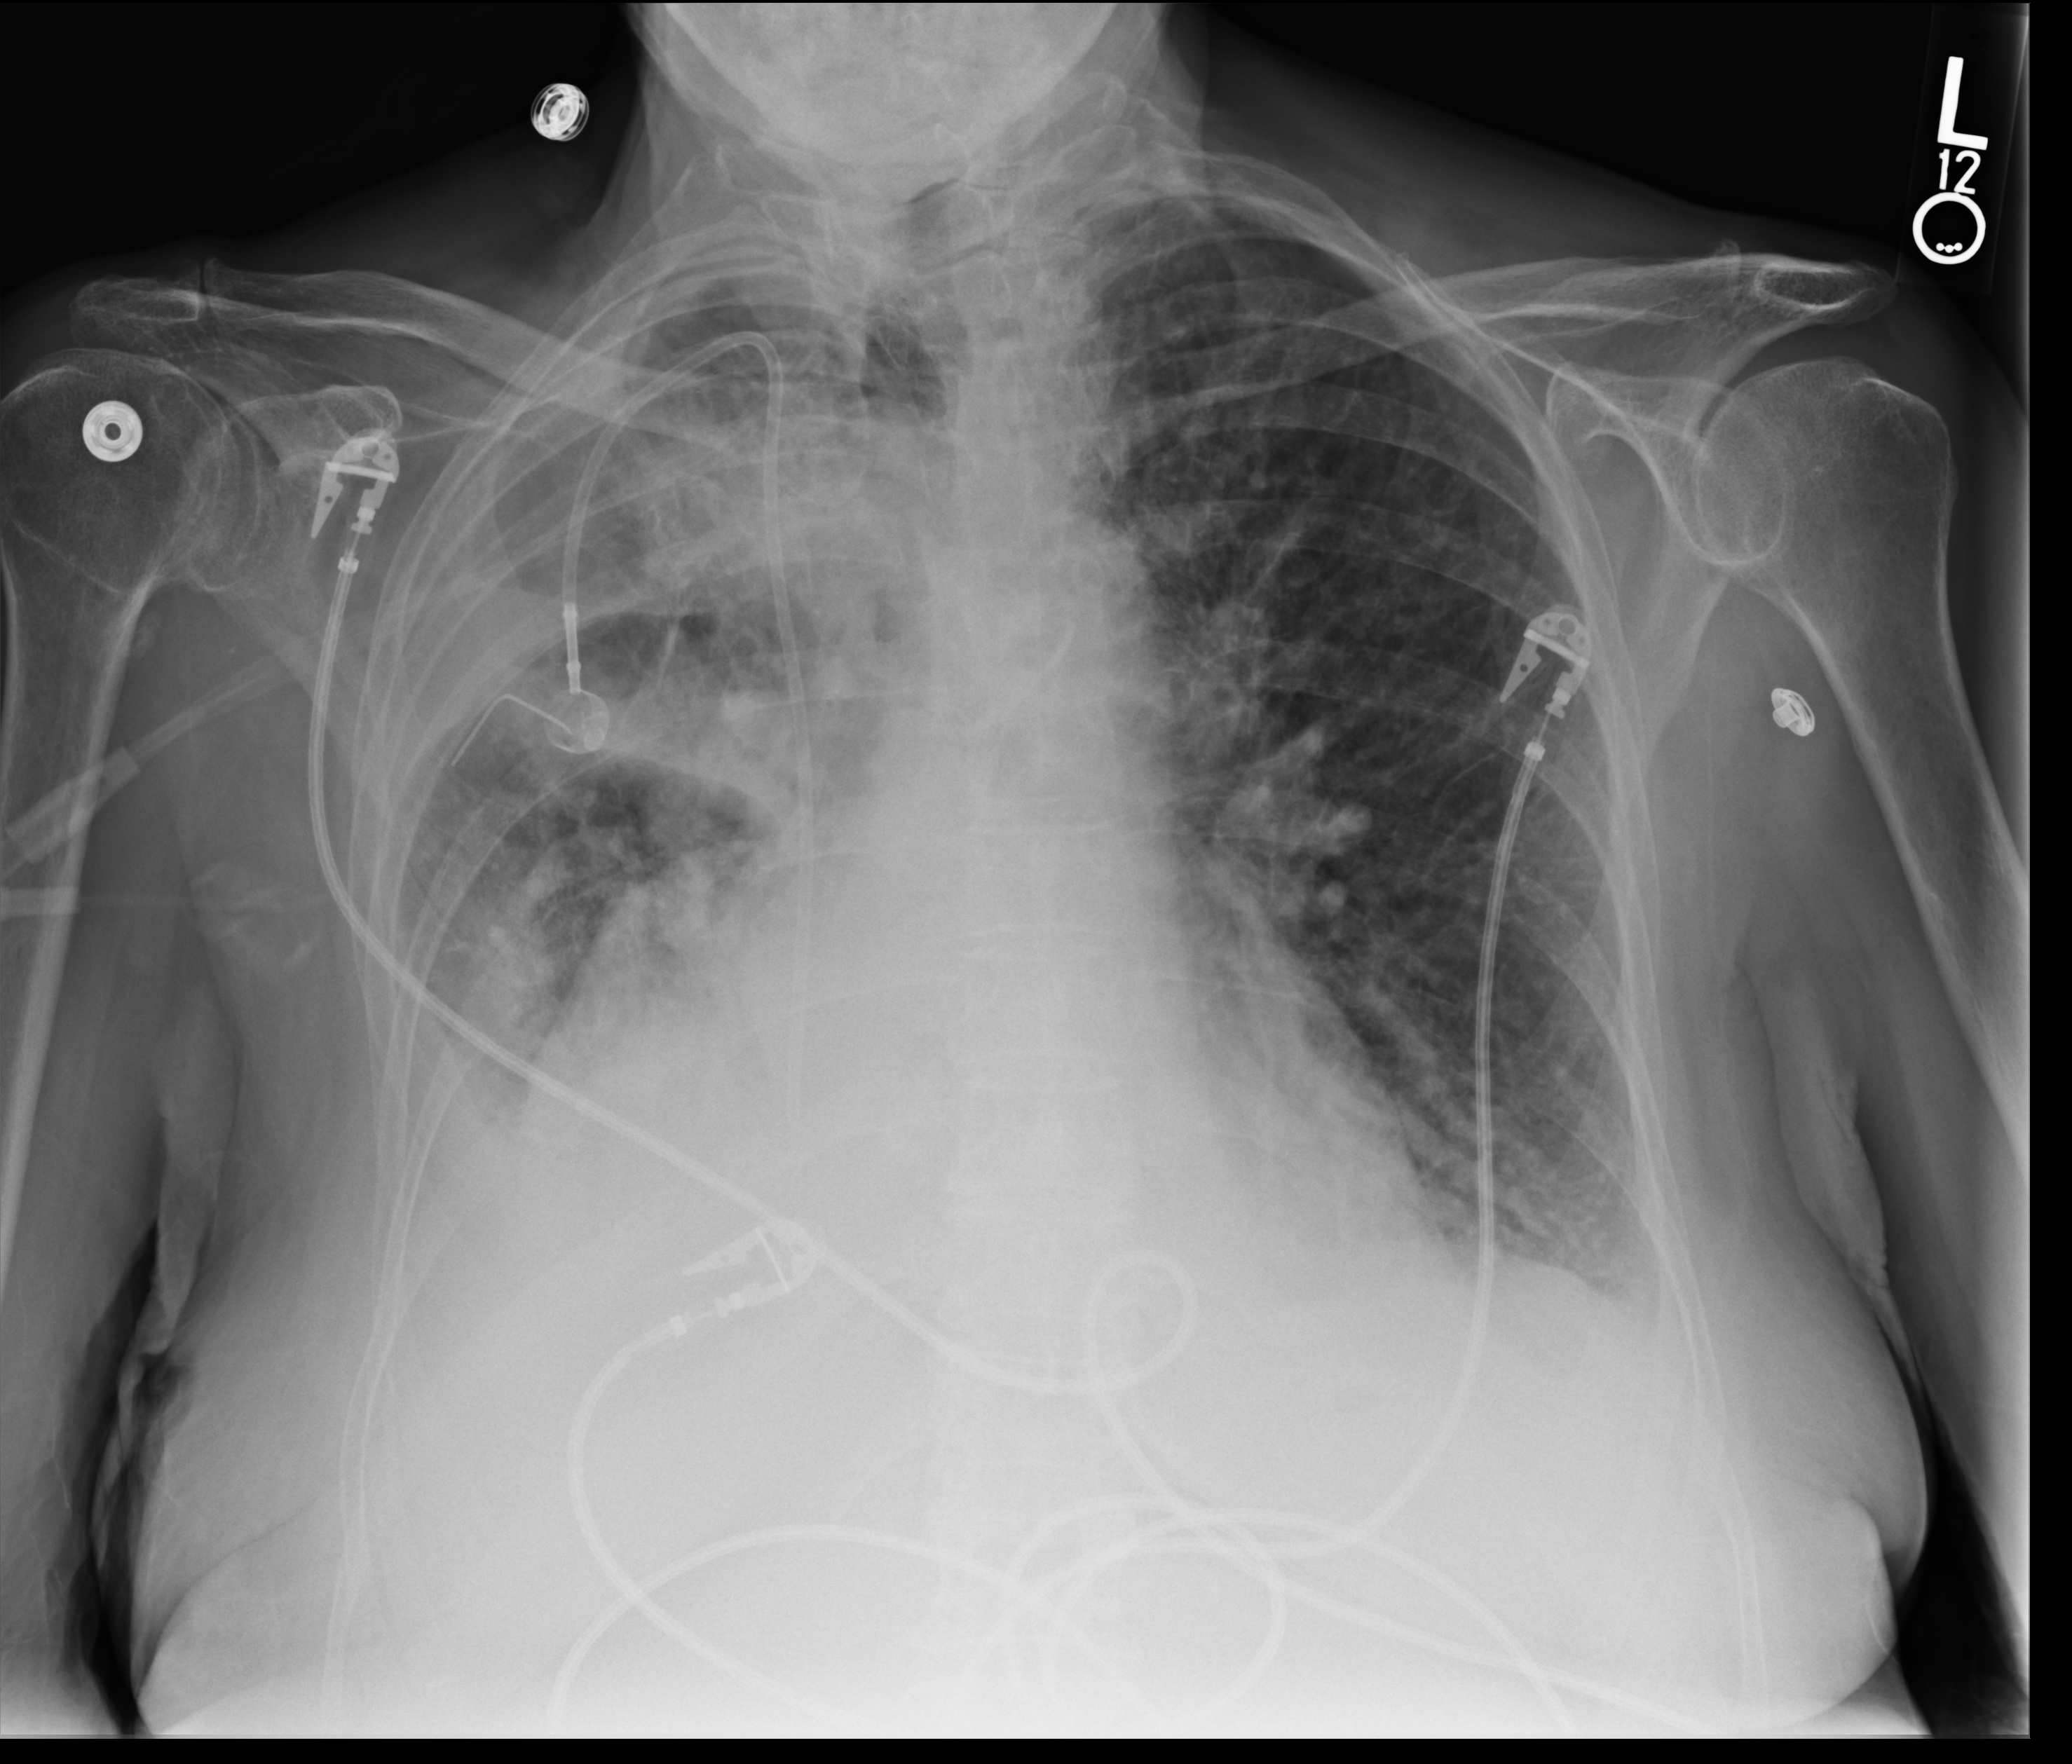
Portable chest radiograph, anteroposterior (AP) projection. Female patient hospitalised with COVID-19, age 60–74 years.
From the hospital-stay record, not from the radiograph (when in the stay this image was taken is not recorded):
- mechanically ventilated during this hospital stay: no